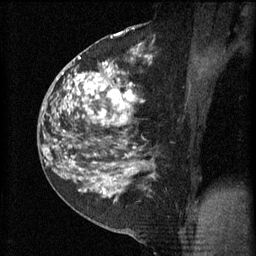
Breast MRI (dynamic contrast-enhanced), one sagittal slice. Slice 27 of 60 in the series (ordered by position). 3 images stored at this slice position (order not interpretable as contrast timing). 1.5 T. TE 4.2 ms, TR 11 ms. 2 mm slice thickness. 256 × 256 image matrix. Patient: female, 52 years.
Structures marked on this image (semi-automatically segmented with operator editing):
- analysis volume of interest (the breast-tissue region the enhancement analysis was run in; not a lesion): bounding box [x1, y1, x2, y2] px = [81, 52, 147, 157]
- tumour enhancement mask (voxels above the 70 % enhancement threshold inside the analysis volume of interest): [81, 58, 138, 157]